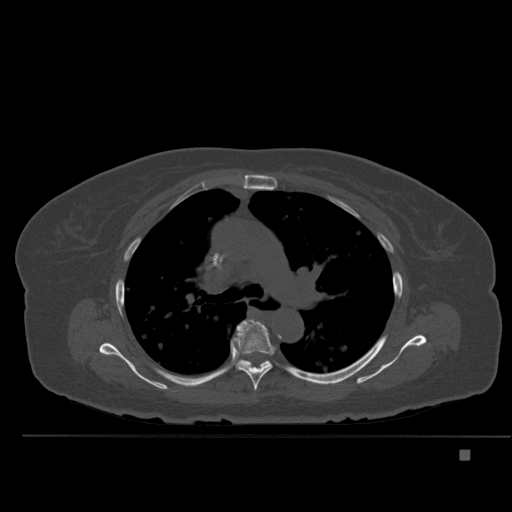
CT including the spine, one axial slice; bone window (W 1800 / L 400 HU); 1.5 mm slice thickness; 512 × 512 image matrix, field of view 422 × 422 mm. Patient: female, 74 years. From the clinical record (not read from this slice): primary cancer: colon.
Outlined on this slice (semi-automatically segmented with operator editing):
- T5 vertebra: box from (x=233, y=319) to (x=274, y=391) px
- T6 vertebra: (x=232, y=340)–(x=271, y=368)